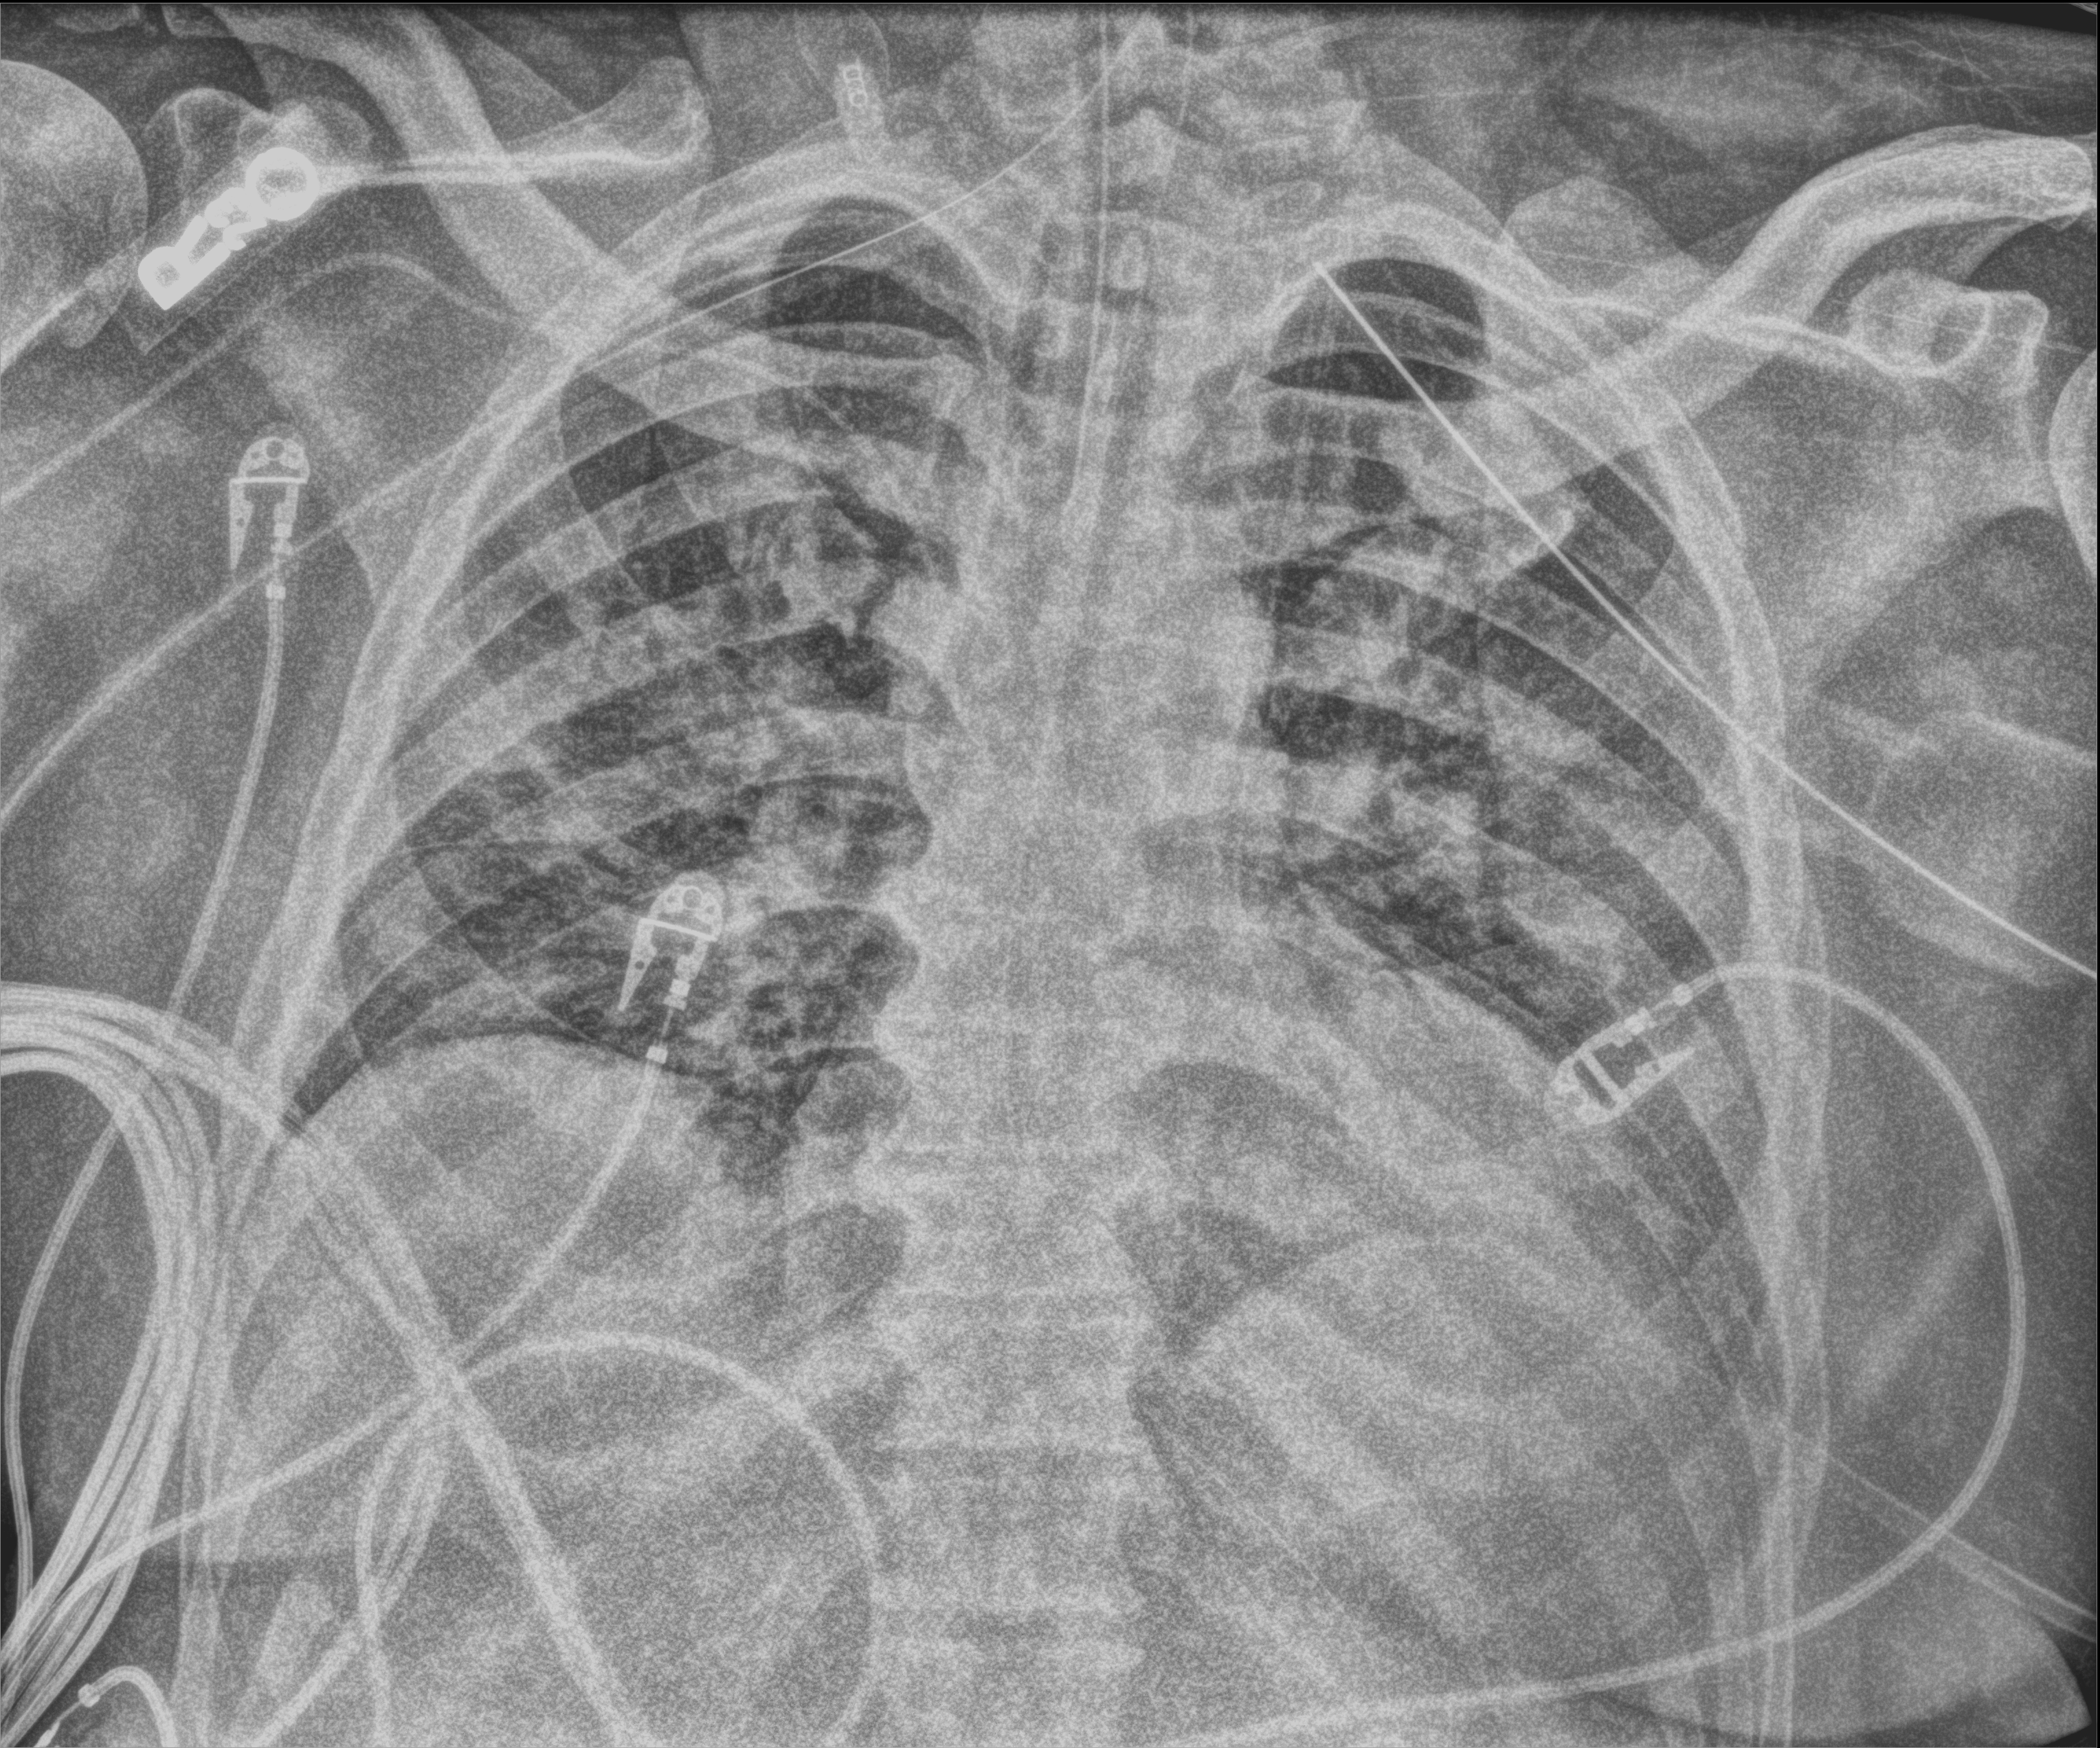
Chest X-ray (portable), anteroposterior (AP) projection. Patient hospitalised with COVID-19; male, aged 18–59 years.
From the hospital-stay record, not from the radiograph (when in the stay this image was taken is not recorded): COPD (admission record): no; admitted to intensive care during this hospital stay: yes; length of hospital stay: 41 days.